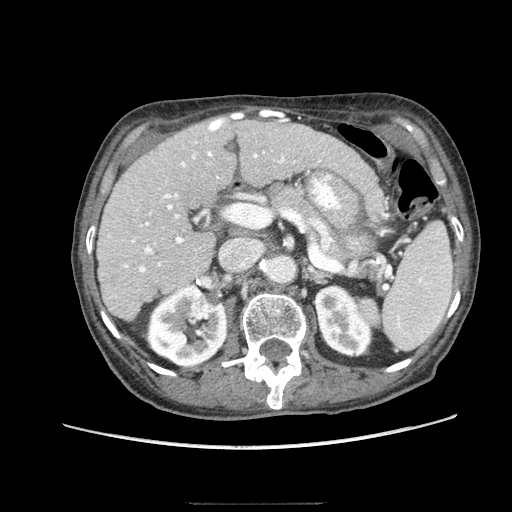
Contrast-enhanced abdominal CT (liver protocol), one axial slice. Soft-tissue window (W 400 / L 40 HU). 2.5 mm slice thickness. 512 × 512 image matrix. From the clinical record (not read from this slice): diagnosis: hepatocellular carcinoma (patient treated with transarterial chemoembolisation; whether this scan precedes or follows treatment is not stated here); TNM stage (as recorded): Stage-I; Child-Pugh class: A; tumour differentiation: moderately differentiated; tumour nodularity: uninodular.
Structures marked on this image (semi-automatic segmentation, software-assisted and operator-edited):
- liver parenchyma outside the tumour (the mass and vessels are separate outlines, so this box may not span the whole liver): box from (x=96, y=114) to (x=333, y=320) px
- liver vessels: (x=123, y=115)–(x=285, y=272)